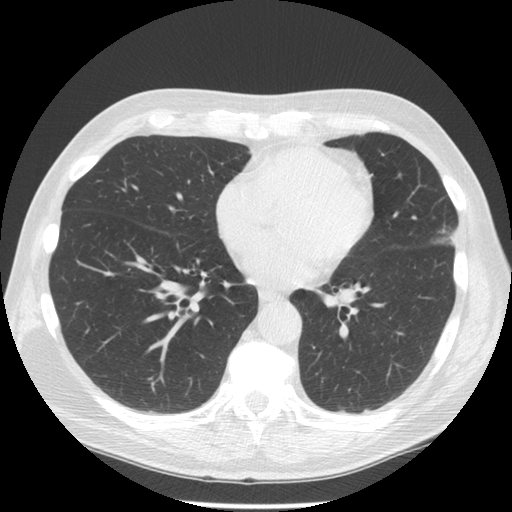
Low-dose screening chest CT, one axial slice. Slice 60 of 134 in the series (ordered by position). 120 kVp. Lung window (W 1500 / L -600 HU). 2.5 mm slice thickness. 512 × 512 image matrix, field of view 350 × 350 mm.
Structures marked on this image (expert manual segmentation):
- lesion 1 (tumor, upper lobe of left lung): box from (x=448, y=232) to (x=456, y=243) px